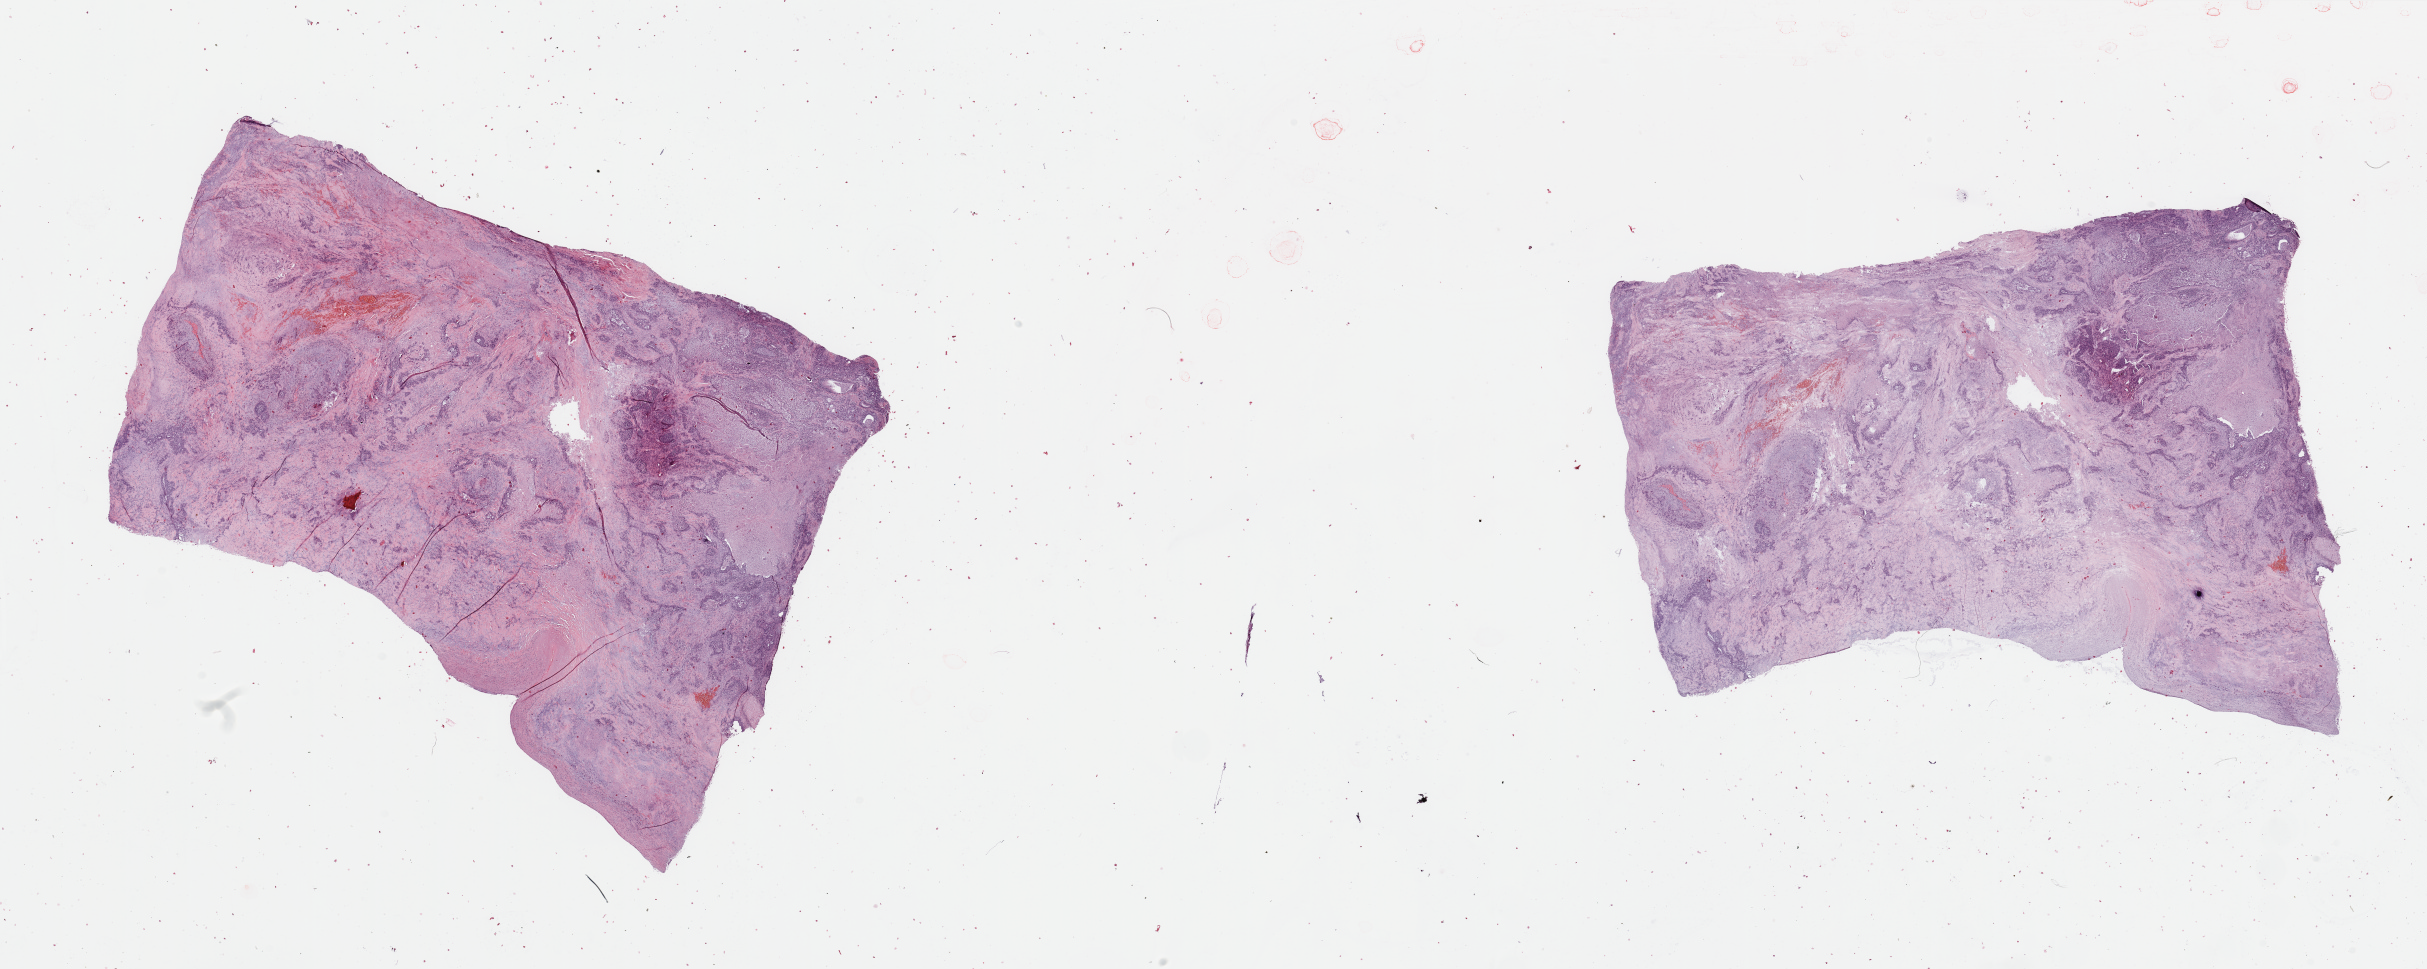
Hematoxylin and eosin (H&E) stained whole-slide image — a low-resolution overview of the entire scanned area, about 38.4 x 15.3 mm (from a 20x scan), tumour tissue sample, lung. Male, 72 y/o. Histologic grade: G3 (poorly differentiated).
AJCC pathologic stage: IIA. Diagnosis: Squamous cell carcinoma, NOS.